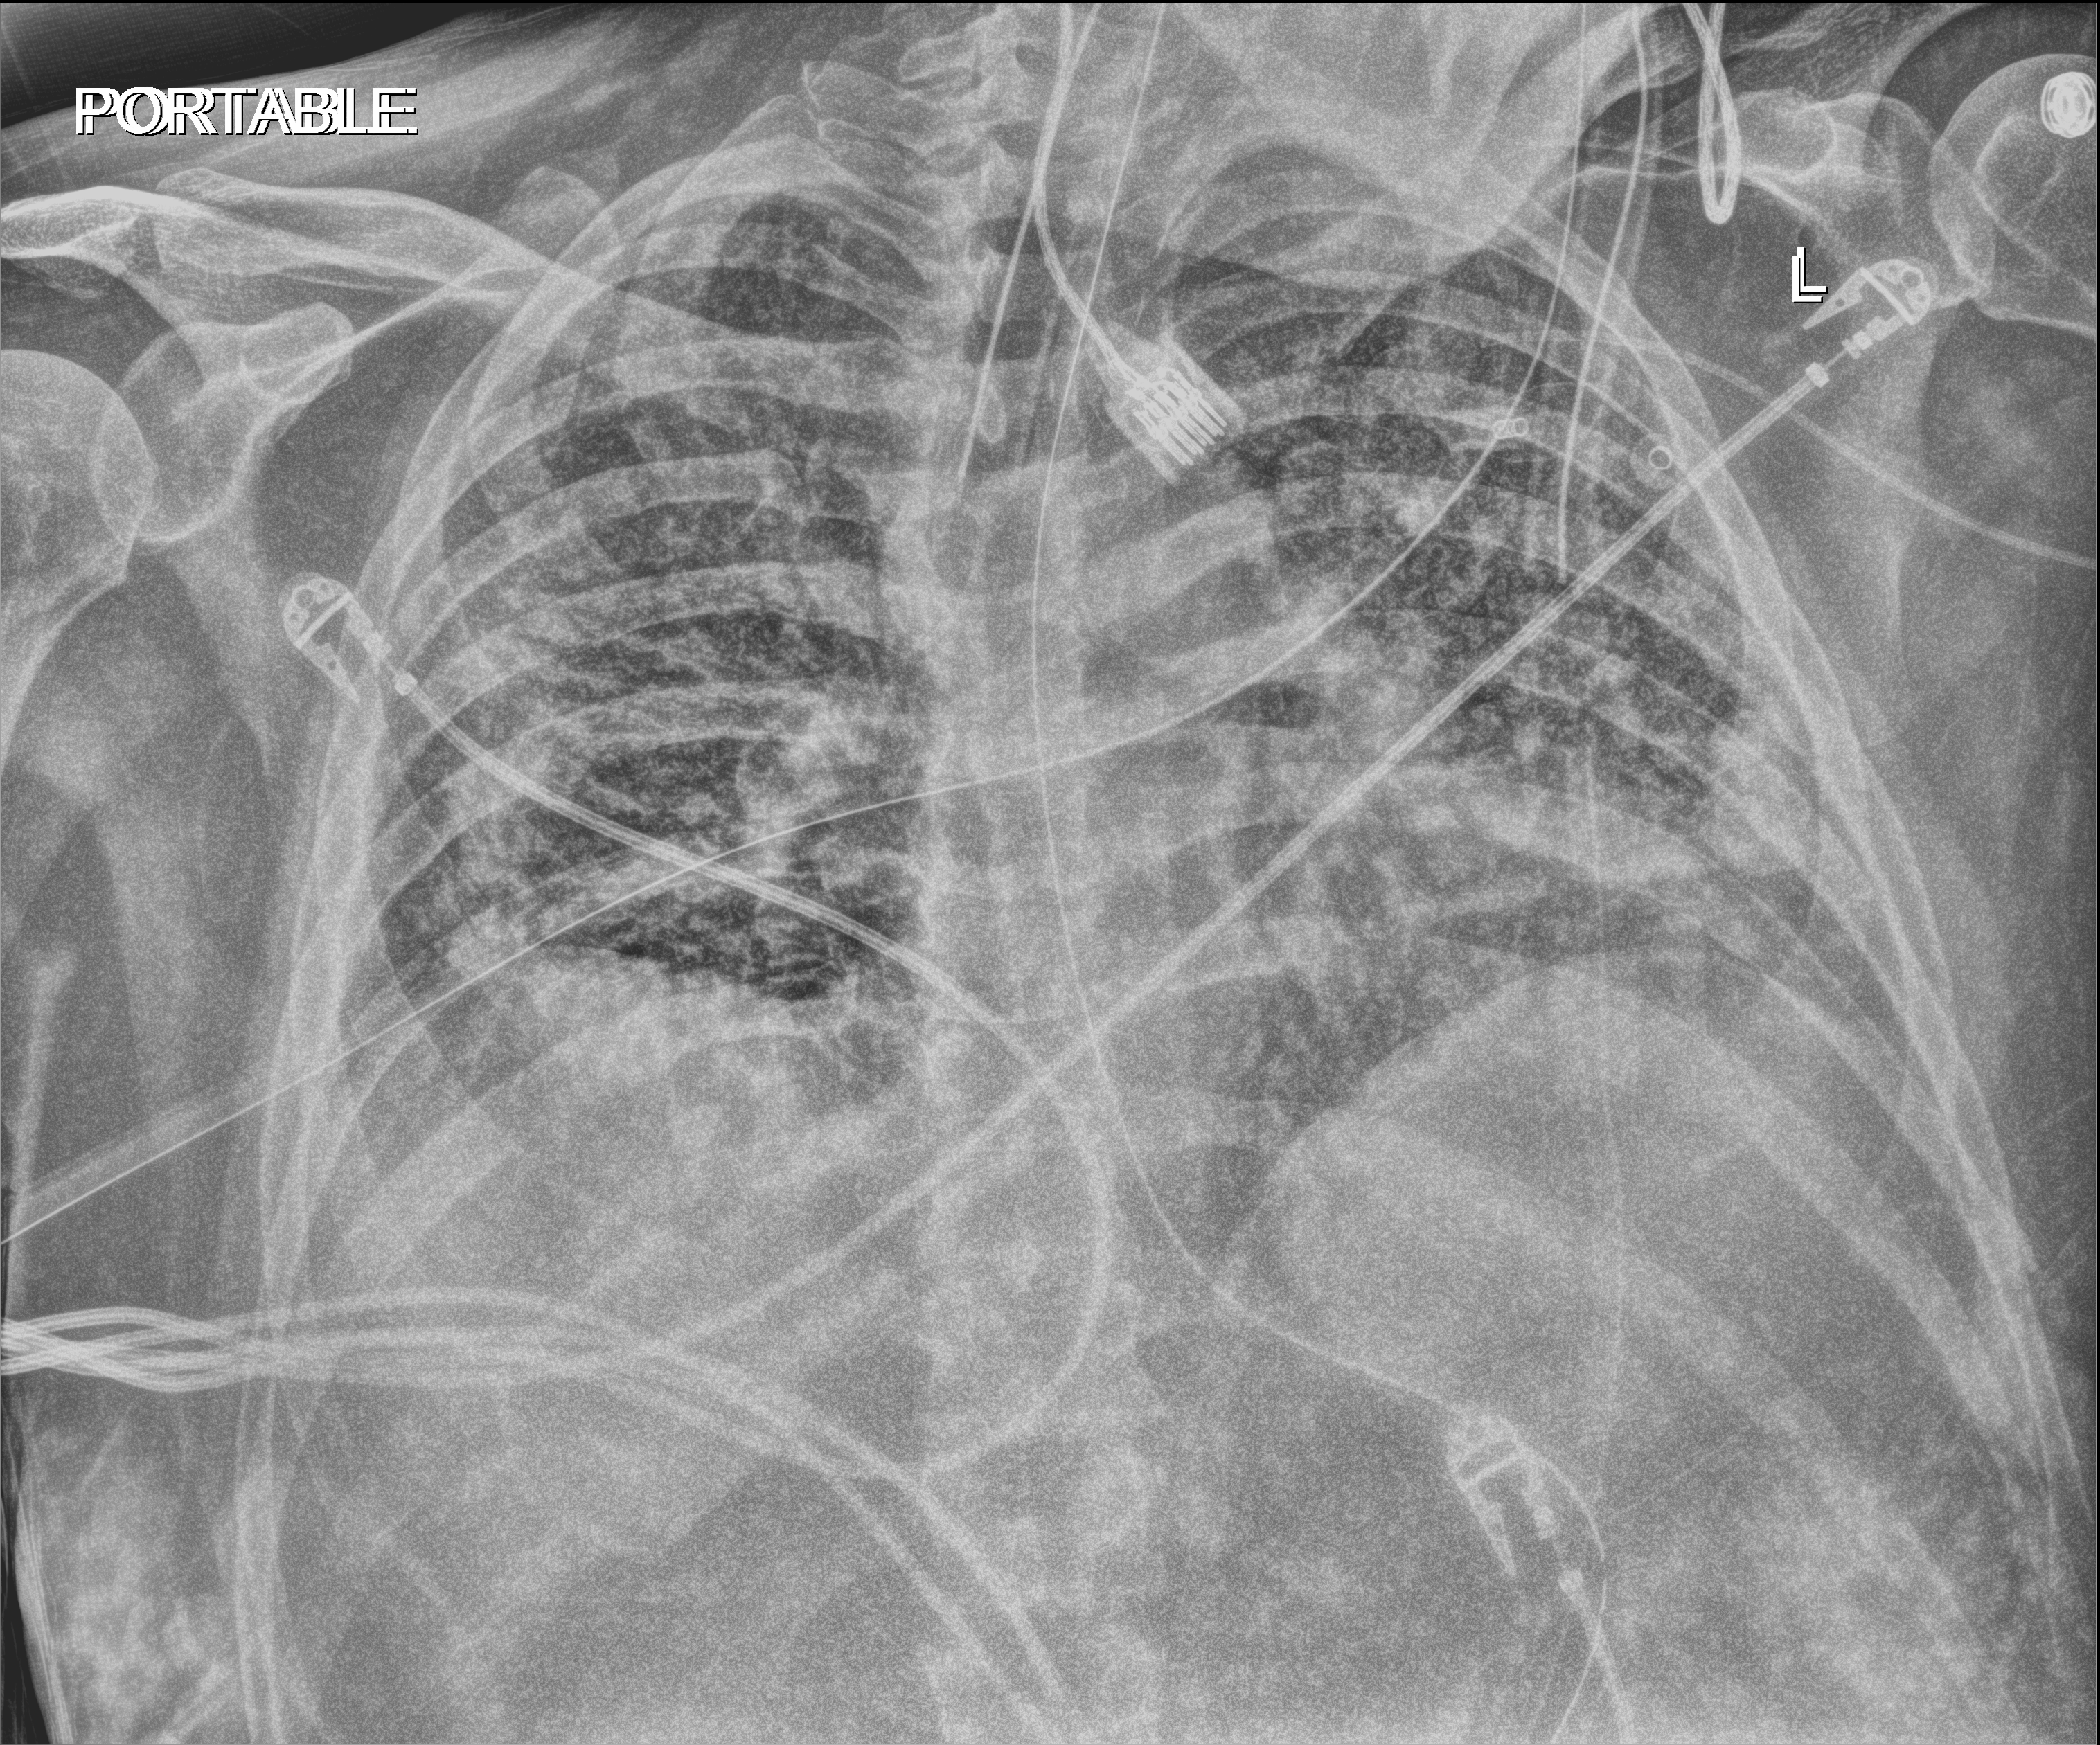
Chest radiograph; anteroposterior (AP) projection. Male patient hospitalised with COVID-19, age 18–59 years.
Admission-level facts for this patient (not findings on this image; timing relative to this image not recorded): admitted to intensive care during this hospital stay: yes; length of hospital stay: 80 days.